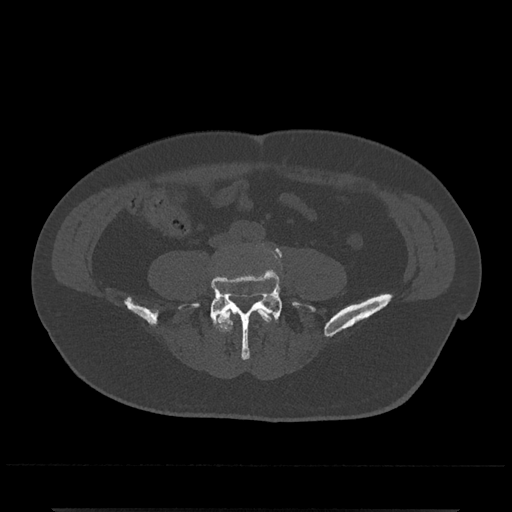
CT including the spine, one axial slice. Position 106 of 797 along the scan axis. Reconstruction kernel Br40s/3. 120 kVp. Bone window (W 1800 / L 400 HU). 0.5 mm slice thickness. 512 × 512 image matrix, field of view 393 × 393 mm. Male patient, age 67 years. Case-level facts recorded for this patient, not image findings: primary cancer: prostate.
Structures marked on this image (semi-automatically segmented with operator editing):
- L4 vertebra: bounding box <216,308,276,332> (left, top, right, bottom; pixels)
- L5 vertebra: <179,244,315,360>